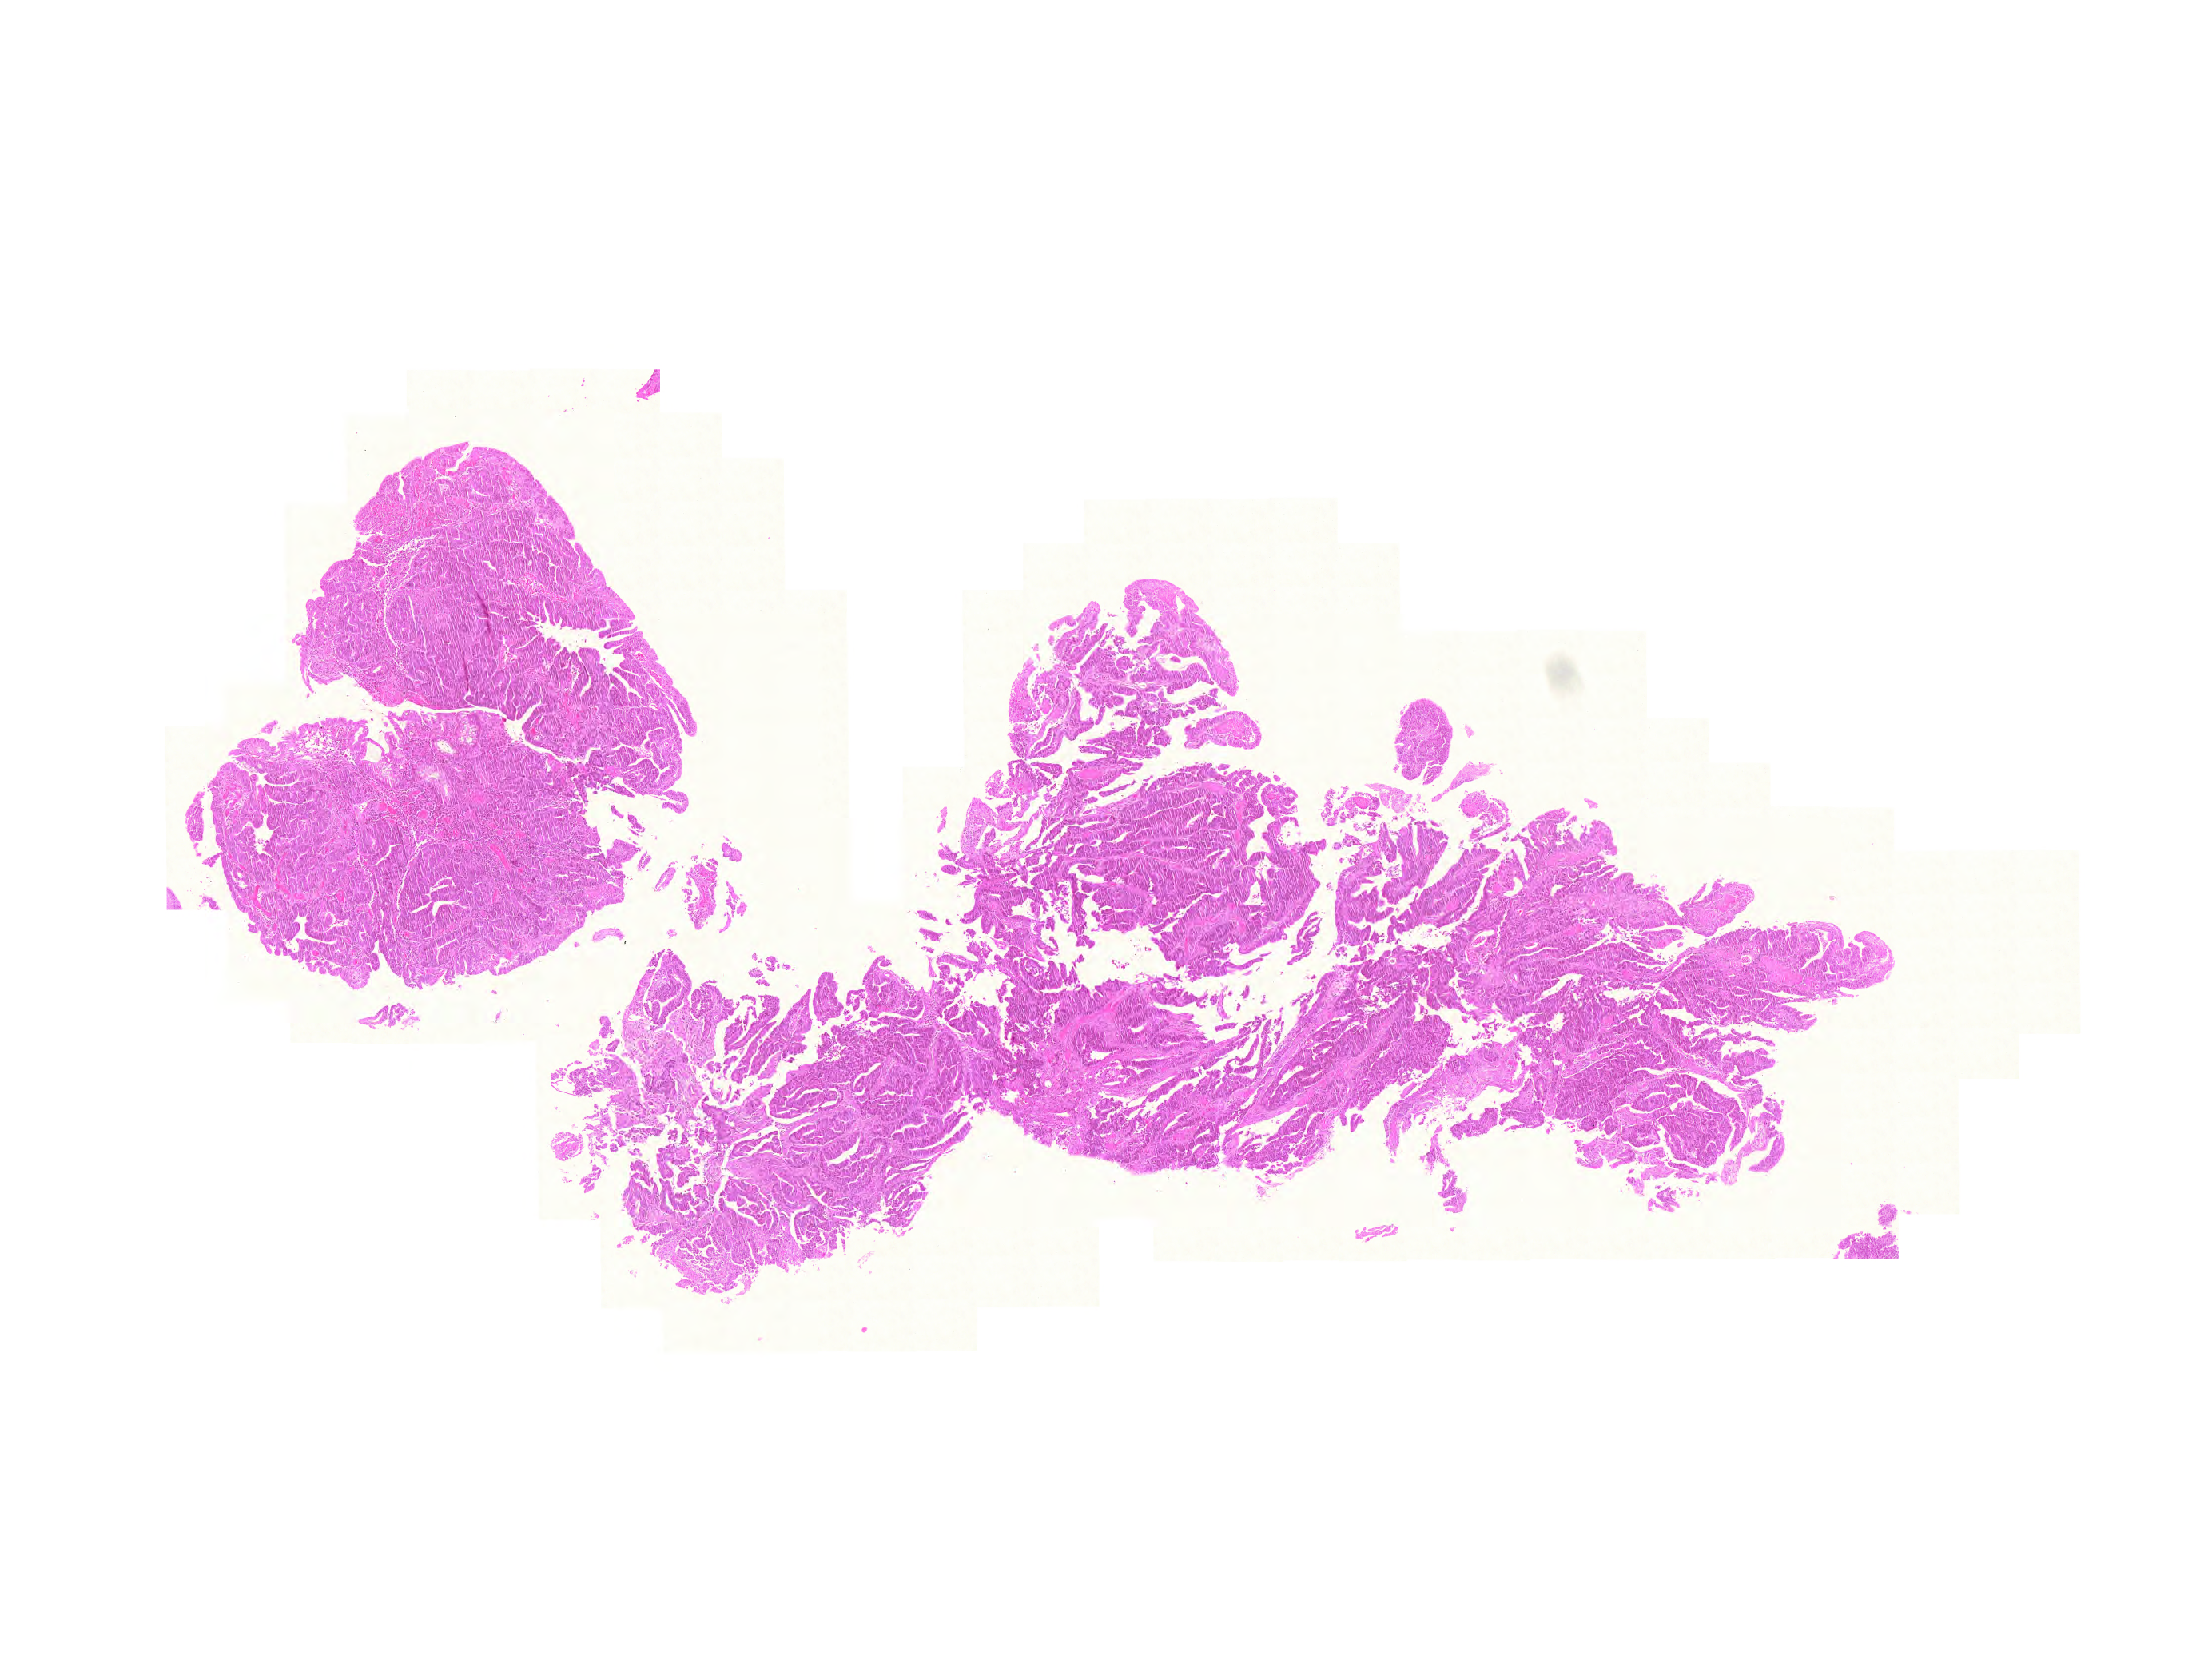
Whole-slide histology image, Hematoxylin and eosin (H&E) stained, shown as a low-resolution overview of the whole scanned area (about 10.3 x 7.8 mm), formalin-fixed paraffin-embedded (FFPE) diagnostic section, sample: primary tumour, rectum. Female, age 78 years at initial diagnosis.
Lymph nodes positive (case pathology): 2 of 25 examined. TNM: T3 N1 M0. AJCC pathologic stage: III. Pathologic diagnosis: Adenocarcinoma, NOS.